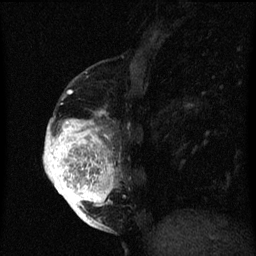
Breast MRI (dynamic contrast-enhanced), one sagittal slice; position 20 of 60 along the scan axis; dynamic contrast-enhanced series, image 2 of 3 at this slice position (ordered by acquisition); 1.5 T; TE 4.2 ms, TR 8 ms; 256 × 256 image matrix, field of view 180 × 180 mm. Patient: female, 56 years.
Annotated regions visible in this slice (semi-automatically segmented with operator editing):
- analysis volume of interest (the breast-tissue region the enhancement analysis was run in; not a lesion): bounding box <44,96,123,219> (left, top, right, bottom; pixels)
- tumour enhancement mask (voxels above the 70 % enhancement threshold inside the analysis volume of interest): <44,112,115,219>